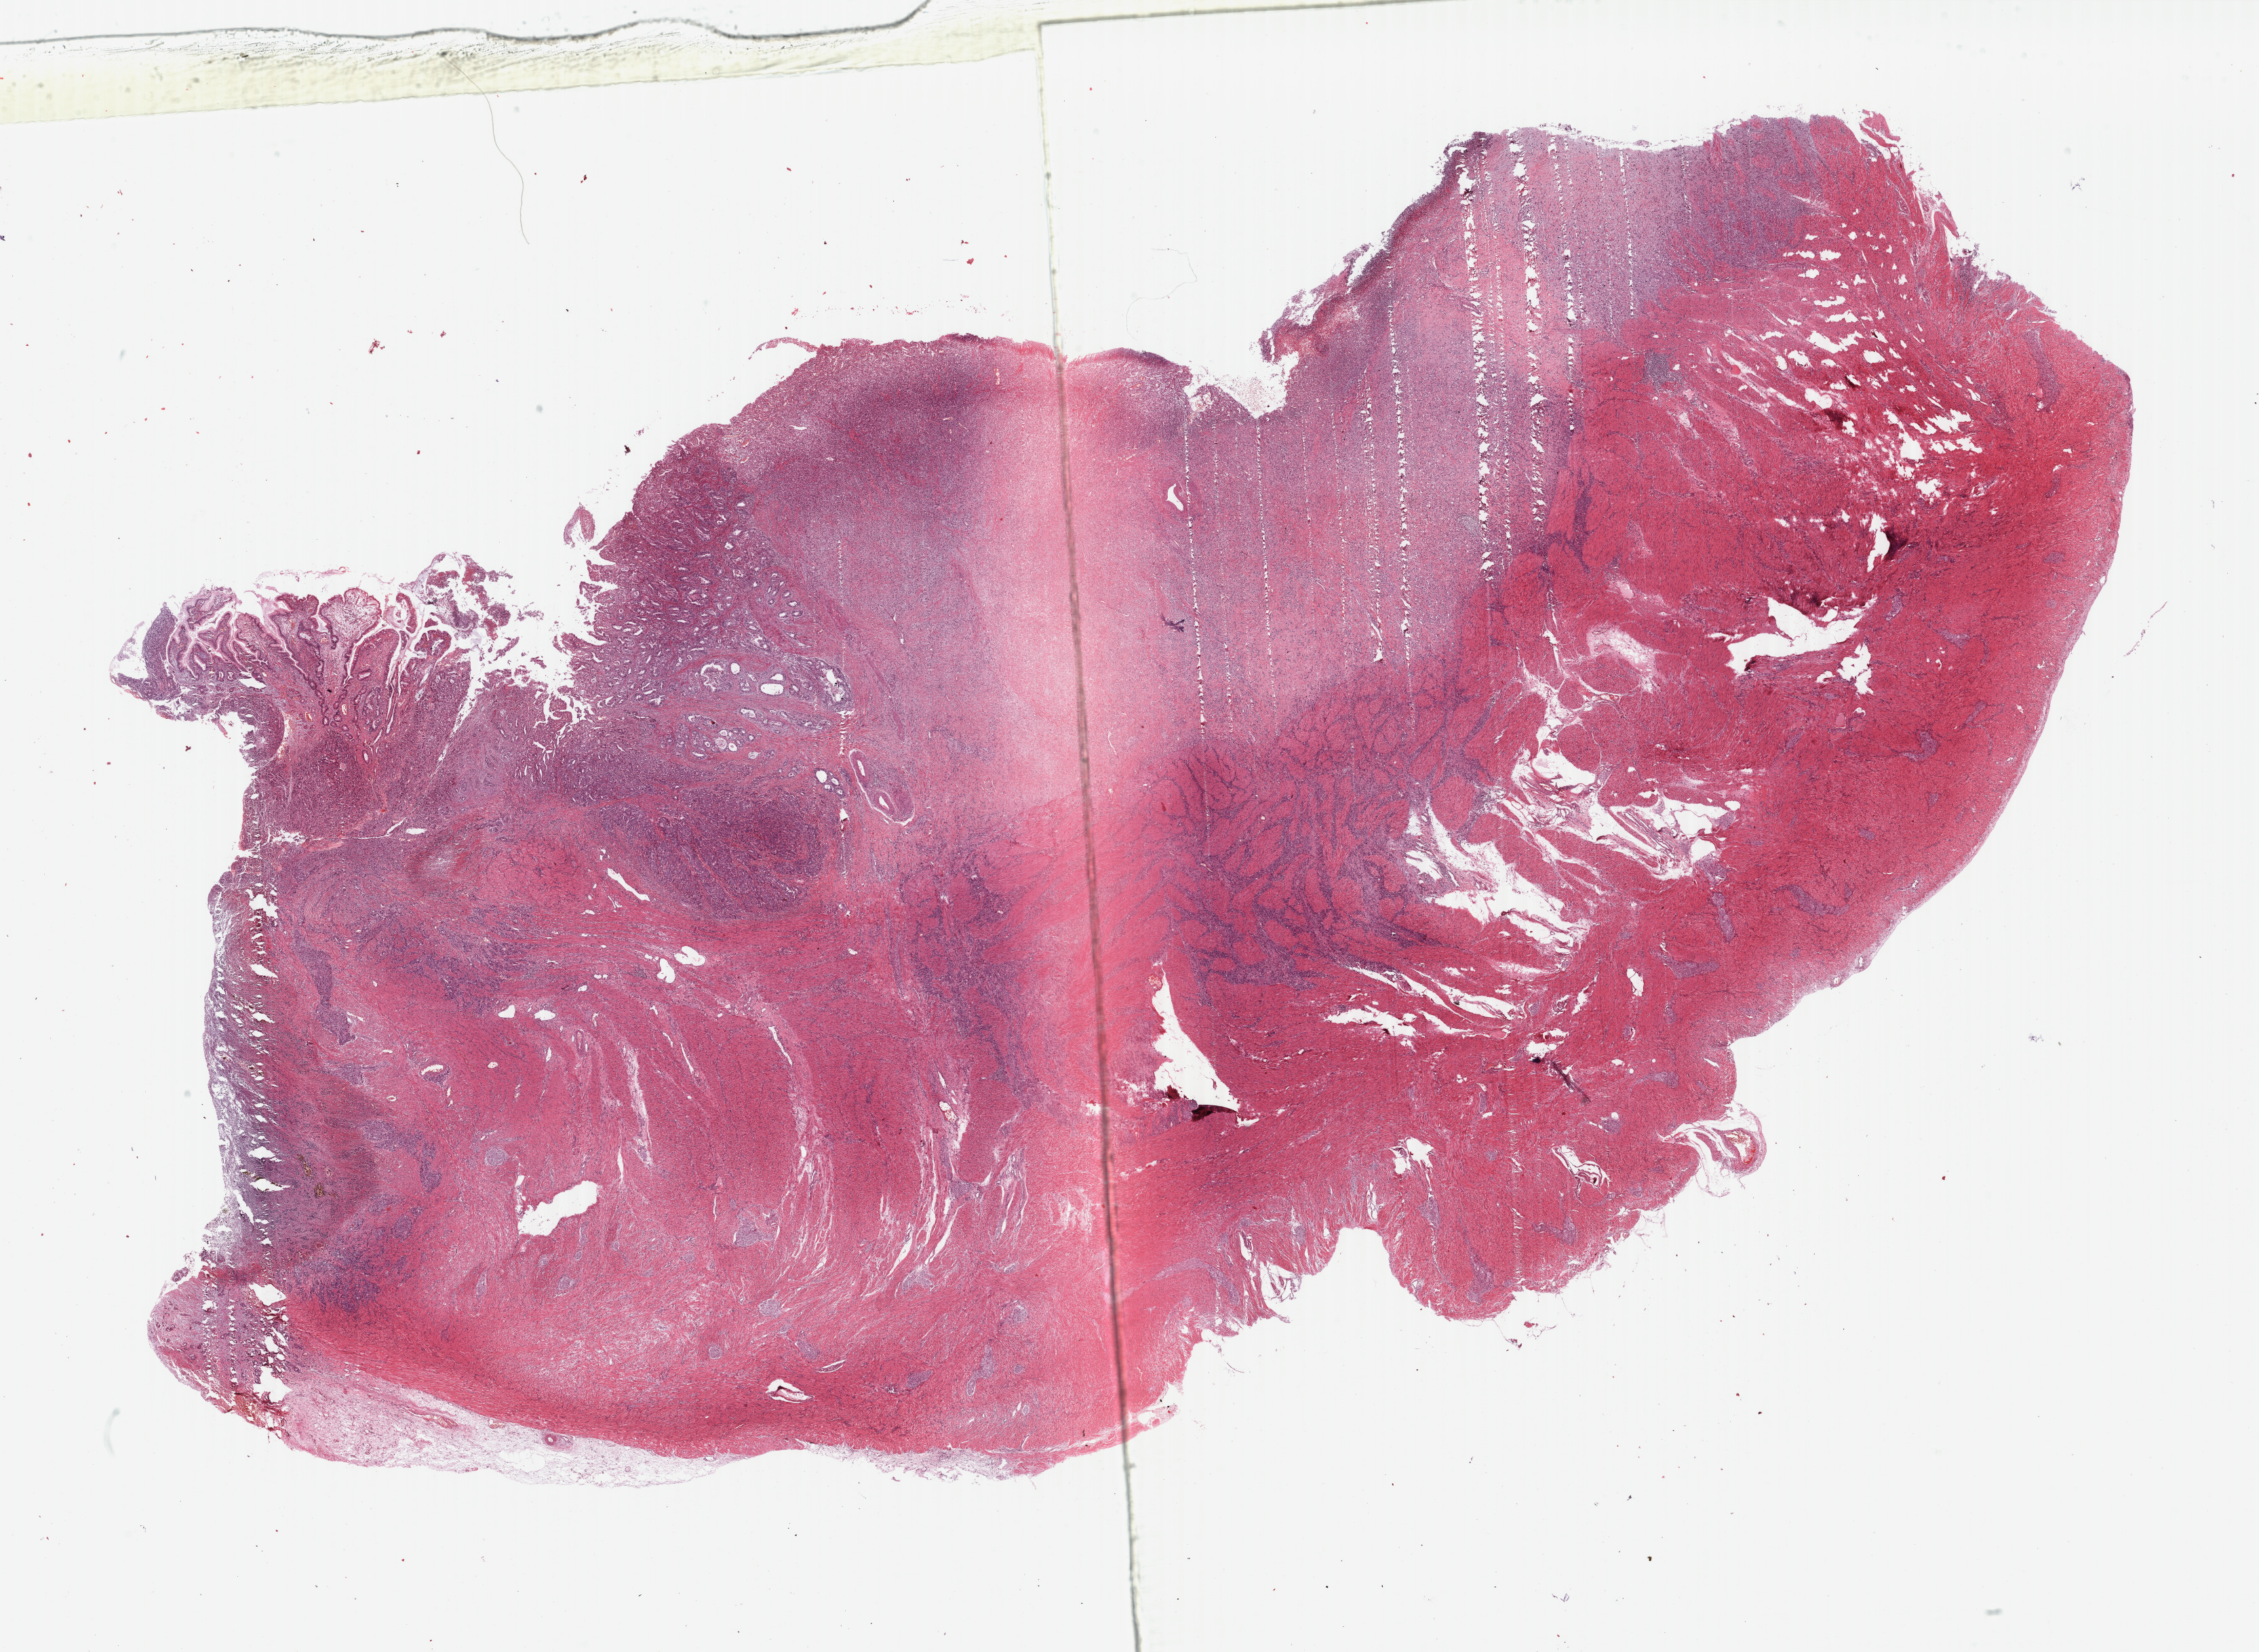
Whole-slide histology image, H&E — shown as a low-resolution overview of the whole scanned area (about 26.4 x 19.3 mm, from a 40x scan). FFPE section. Stomach, primary tumour sample. Patient: male, age at initial diagnosis 51 years.
Histologic diagnosis: Carcinoma, diffuse type (gastric antrum).